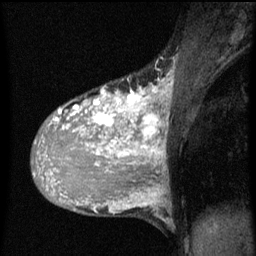
Breast MRI (dynamic contrast-enhanced), one sagittal slice; slice 32 of 60 in the series (ordered by position); dynamic contrast-enhanced series, image 2 of 3 at this slice position (ordered by acquisition); 1.5 T; TE 4.2 ms, TR 8 ms; 2 mm slice thickness; 256 × 256 image matrix, field of view 180 × 180 mm. Patient: female, 36 years.
Outlined on this slice (semi-automatically segmented with operator editing):
- analysis volume of interest (the breast-tissue region the enhancement analysis was run in; not a lesion): bounding box [x1, y1, x2, y2] px = [34, 80, 167, 161]
- tumour enhancement mask (voxels above the 70 % enhancement threshold inside the analysis volume of interest): [36, 80, 167, 161]